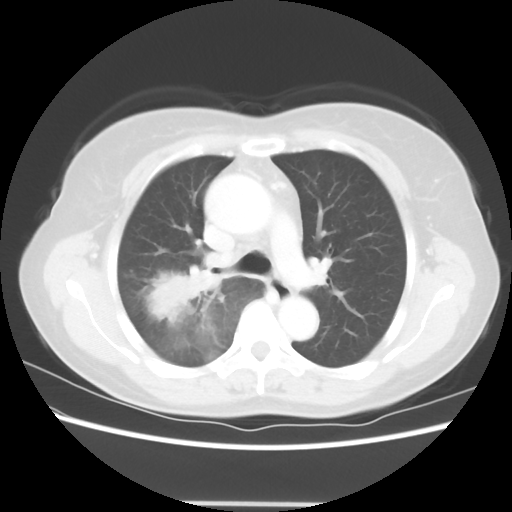
Chest CT, one axial slice. Position 39 of 56 along the scan axis. Reconstruction kernel STANDARD. Lung window (W 1500 / L -600 HU). 512 × 512 image matrix, field of view 360 × 360 mm. Patient: female, 55 years. From the clinical record (not read from this slice): clinical TNM (as recorded): T2 N1 M0.
Structures marked on this image (rectangle marked by the reading radiologist):
- lung tumour (recorded histology: adenocarcinoma): bounding box <131,252,237,346> (left, top, right, bottom; pixels)